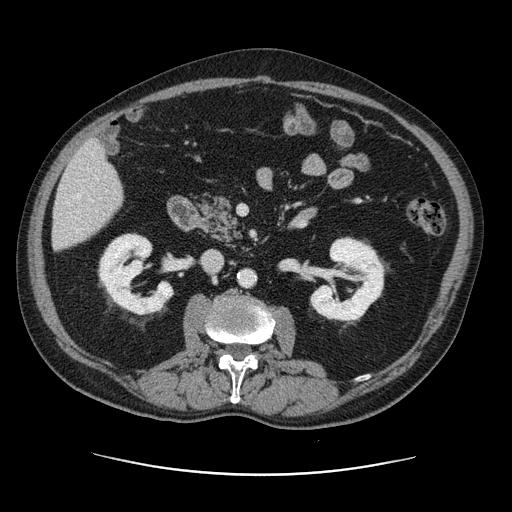
Contrast-enhanced abdominal CT, one axial slice; slice 45 of 141 in the series (ordered by position); intravenous contrast given; soft-tissue window (W 400 / L 40 HU); 512 × 512 image matrix. Male patient, age 72 years. From the clinical record (not read from this slice): diagnosis: colorectal cancer liver metastases, imaged before liver resection; multiple liver metastases: yes; largest metastasis: 5.4 cm; disease in both lobes: yes.
Annotated regions visible in this slice (manually delineated by an expert):
- hepatic veins: box from (x=66, y=194) to (x=93, y=203) px
- liver: (x=53, y=142)–(x=123, y=250)
- planned liver remnant (the part of the liver to remain after resection): (x=53, y=157)–(x=123, y=250)
- portal vein (with intrahepatic branches): (x=76, y=229)–(x=82, y=232)